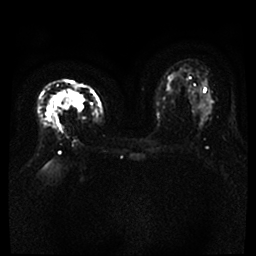
Breast MRI, one axial slice; slice 20 of 46 in the series (ordered by position); diffusion-weighted series; image 2 of 4 stored at this slice position (different b-values; order by instance number); 1.5 T; 4 mm slice thickness; 256 × 256 image matrix, field of view 360 × 360 mm. Female patient.
Annotated regions visible in this slice (expert manual segmentation):
- tumour on diffusion-weighted imaging: bounding box [x1, y1, x2, y2] px = [46, 90, 83, 117]